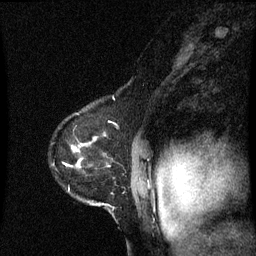
Breast MRI (dynamic contrast-enhanced), one sagittal slice; slice 50 of 60 in the series (ordered by position); dynamic contrast-enhanced series, image 2 of 3 at this slice position (ordered by acquisition); 1.5 T; TE 4.2 ms, TR 8.9 ms; 256 × 256 image matrix, field of view 200 × 200 mm. Patient: female, 53 years. From the clinical record (not read from this slice): setting: breast cancer imaged before/during neoadjuvant chemotherapy; receptor status: HR-positive, HER2-negative.
Annotated regions visible in this slice (semi-automatically segmented with operator editing):
- analysis volume of interest (the breast-tissue region the enhancement analysis was run in; not a lesion): bounding box (x1, y1, x2, y2) in pixels: (52, 114, 145, 217)
- tumour enhancement mask (voxels above the 70 % enhancement threshold inside the analysis volume of interest): (64, 150, 75, 165)